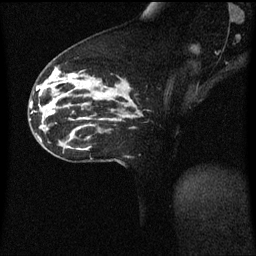
Breast MRI (dynamic contrast-enhanced), one sagittal slice. Slice 33 of 60 in the series (ordered by position). Dynamic contrast-enhanced series, image 2 of 3 at this slice position (ordered by acquisition). 1.5 T. TE 4.2 ms, TR 8.4 ms. 2 mm slice thickness. 256 × 256 image matrix. Patient: female, 33 years. From the clinical record (not read from this slice): setting: breast cancer imaged before/during neoadjuvant chemotherapy; receptor status: triple-negative.
Structures marked on this image (semi-automatic segmentation, software-assisted and operator-edited):
- analysis volume of interest (the breast-tissue region the enhancement analysis was run in; not a lesion): bounding box [x1, y1, x2, y2] px = [76, 70, 123, 113]
- tumour enhancement mask (voxels above the 70 % enhancement threshold inside the analysis volume of interest): [96, 88, 106, 97]